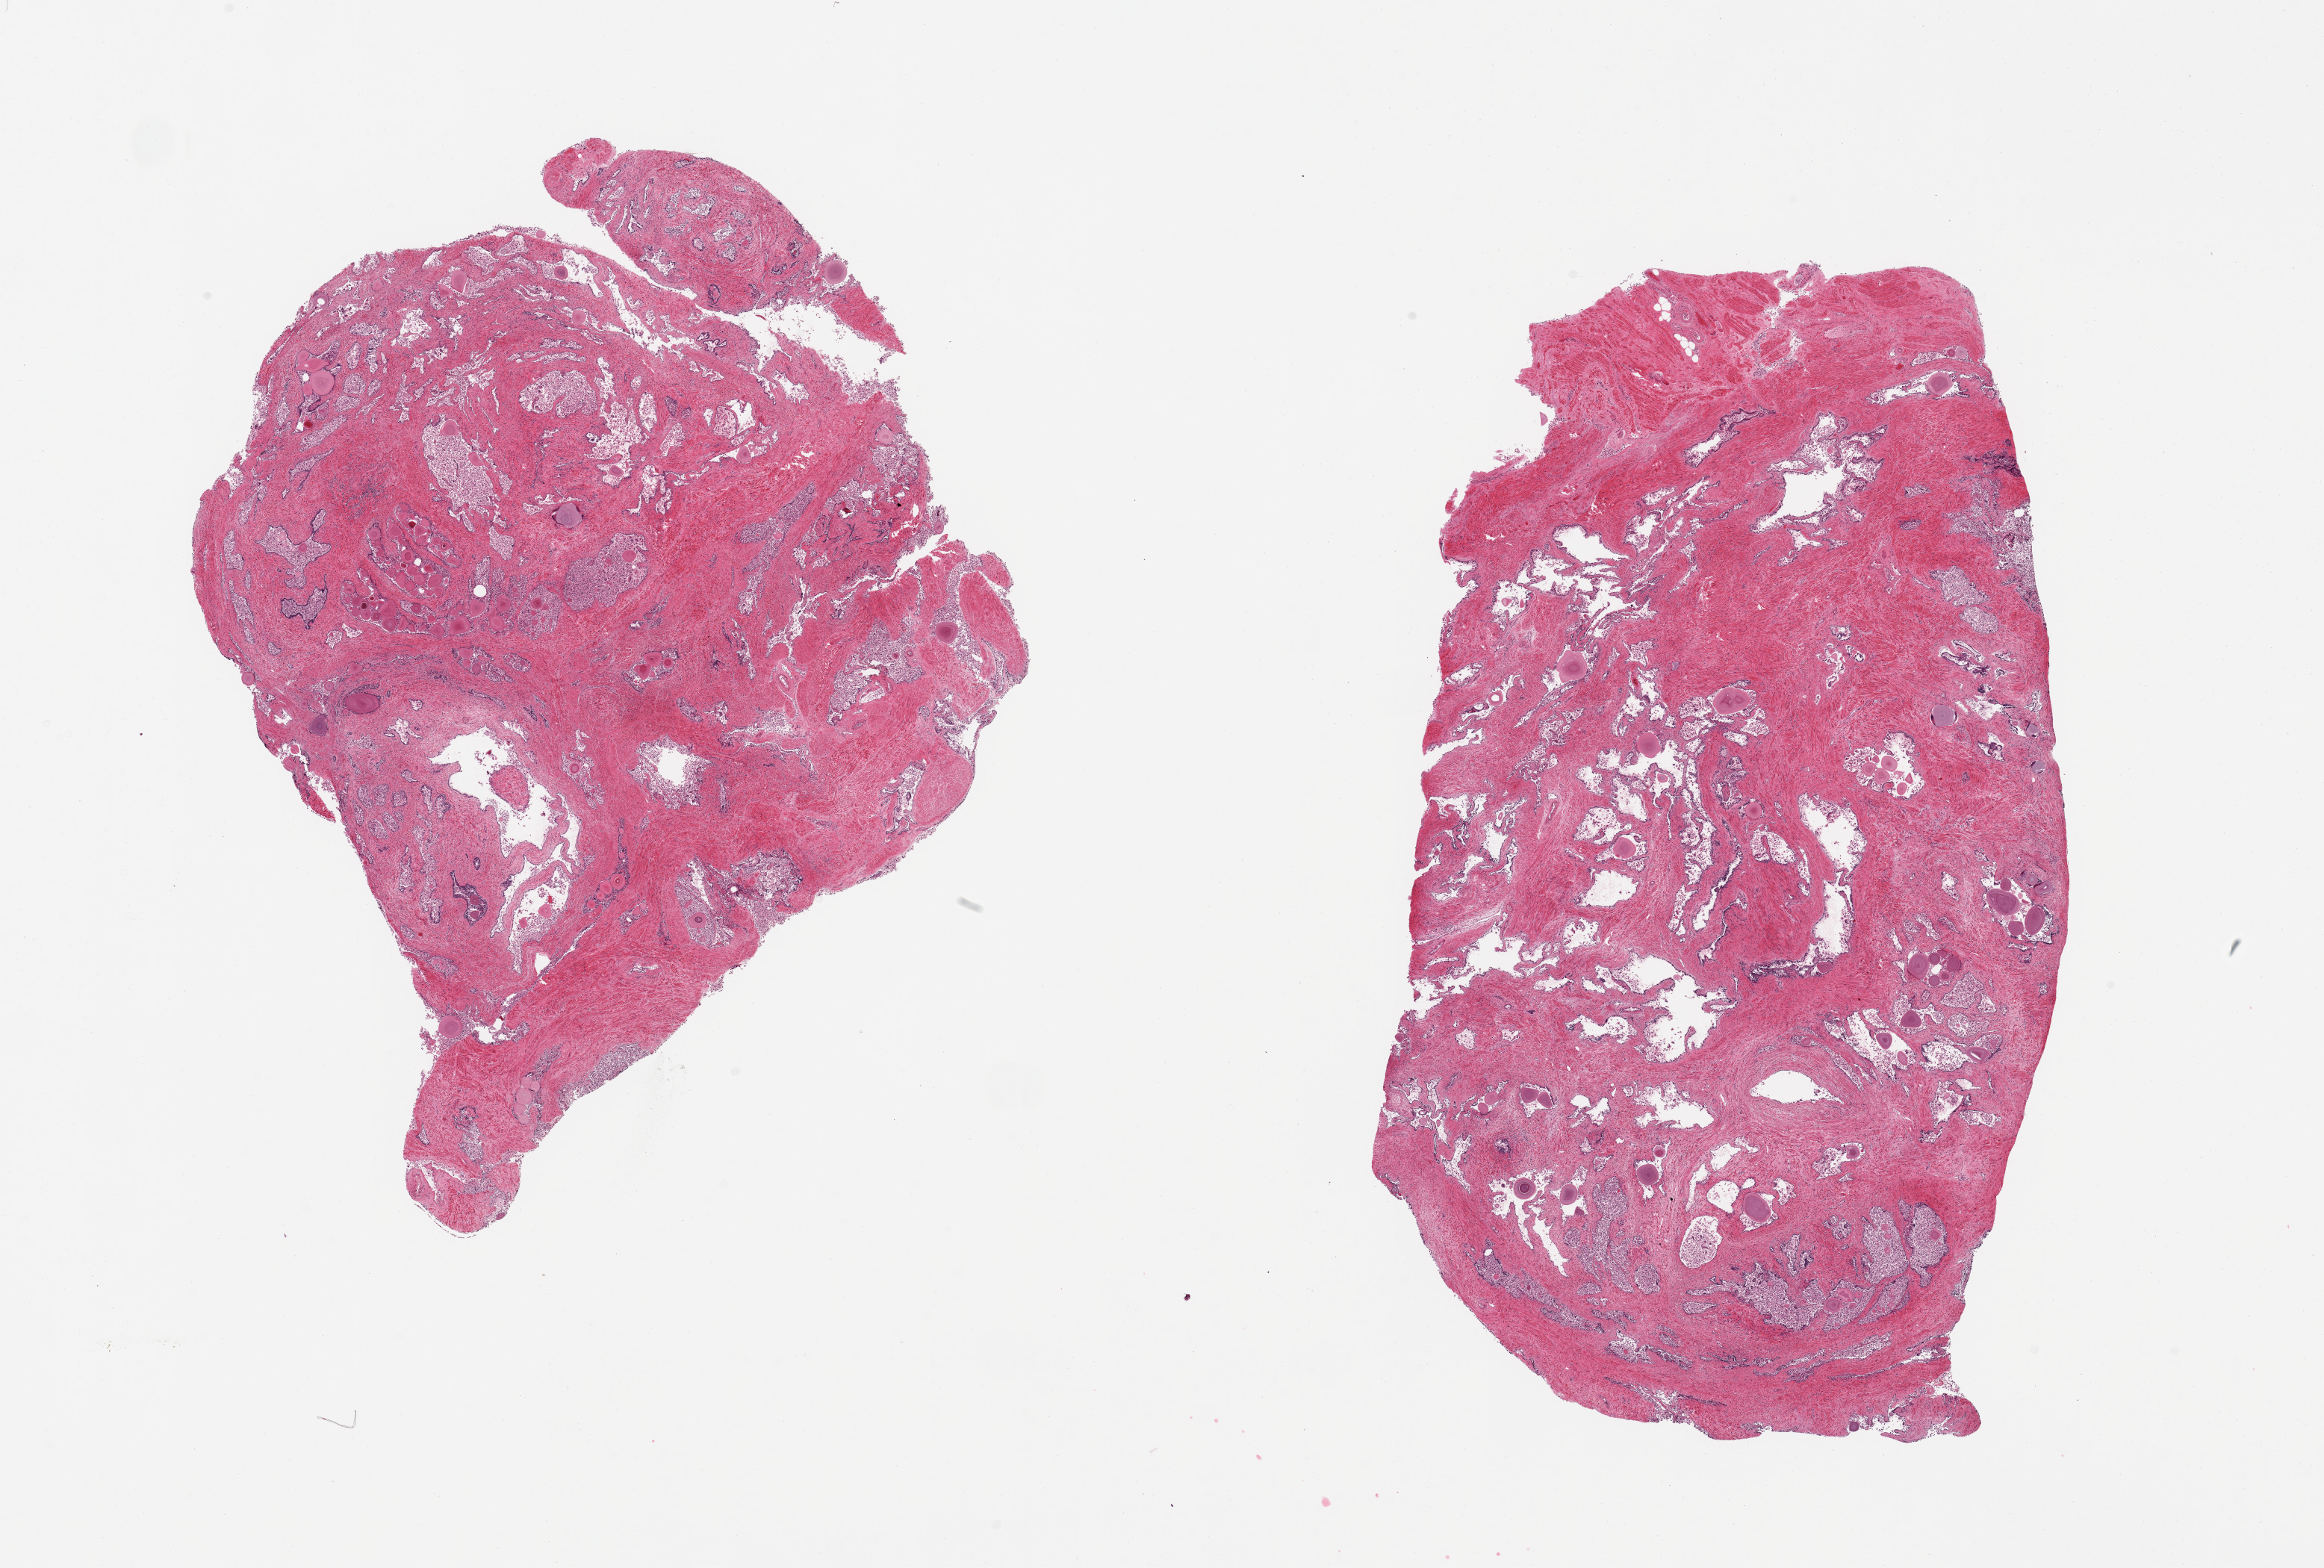
Digitized H&E-stained section, brightfield, low-resolution overview of the scanned area, about 24.6 x 16.6 mm; PAXgene-fixed, paraffin-embedded tissue; section of prostate (target tissue); tissue donor sample. Donor sex: male.
Reviewer comment on this tissue sample: 2 pieces; fibrovascular stroma and glandular component with diffusely sloughed epithelium and numerous corpora amylacea, stroma intact.